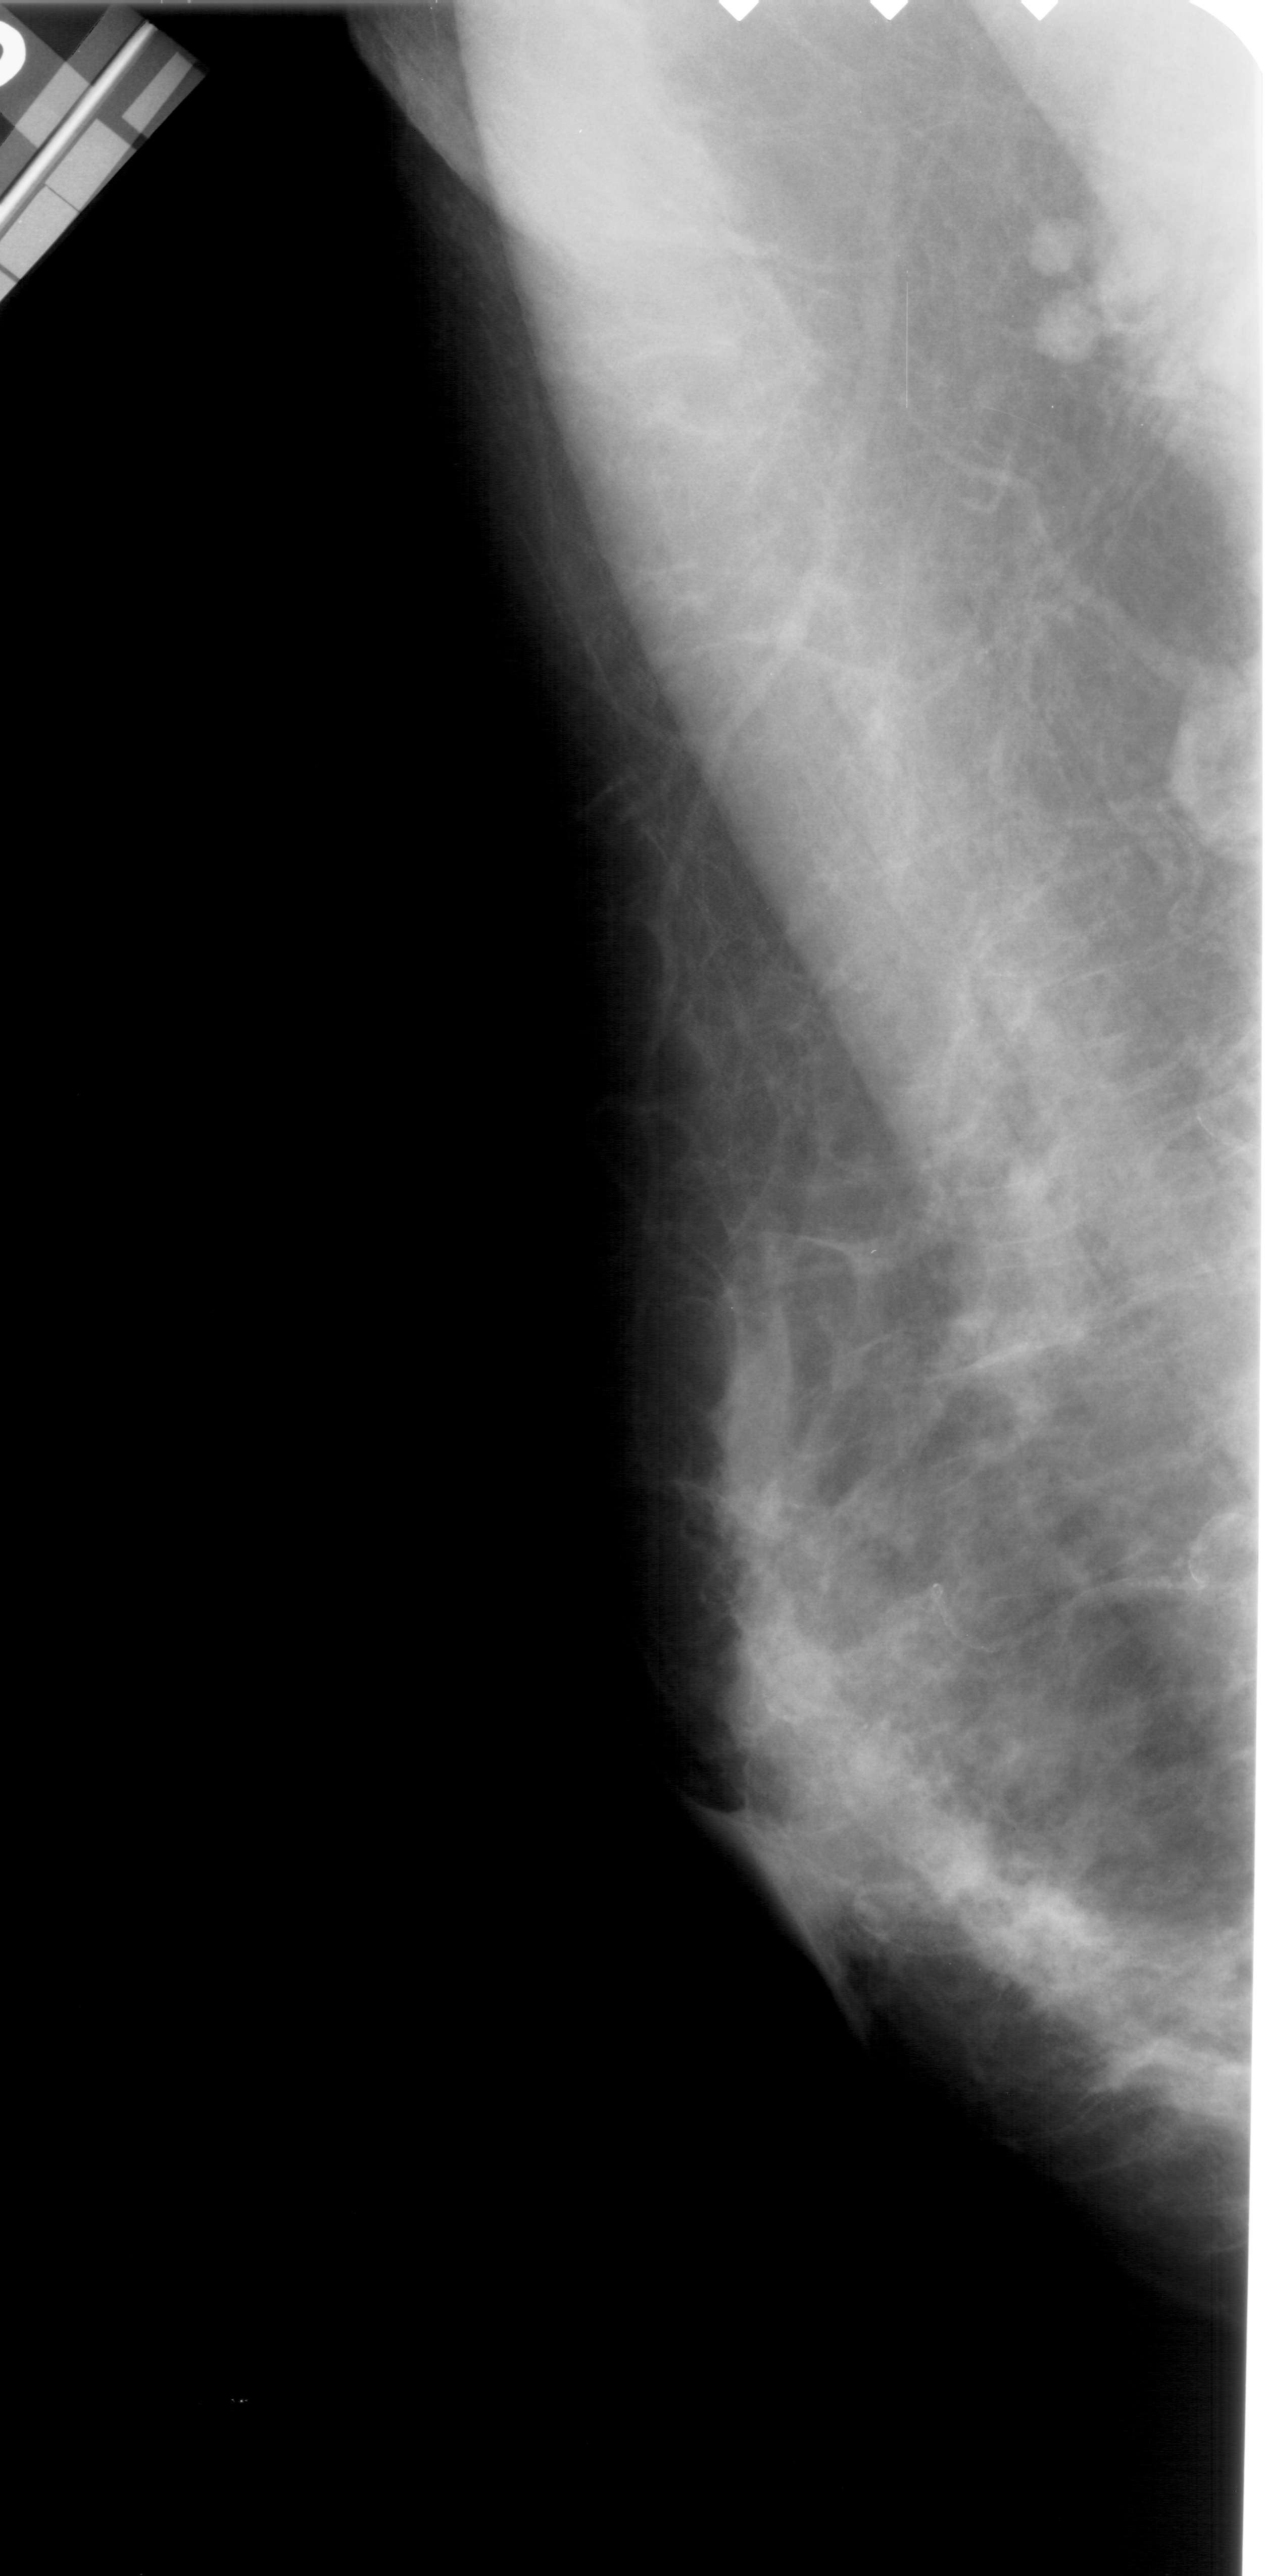
Mammogram (digitized film). Left breast. Mediolateral oblique (MLO) view. 1266 × 2576 image matrix.
Expert-marked regions of interest on this image (one box per marked abnormality):
- mass, shape irregular, margins spiculated; BI-RADS assessment category 5; pathology (as recorded): benign: box from (x=964, y=1851) to (x=1128, y=1994) px